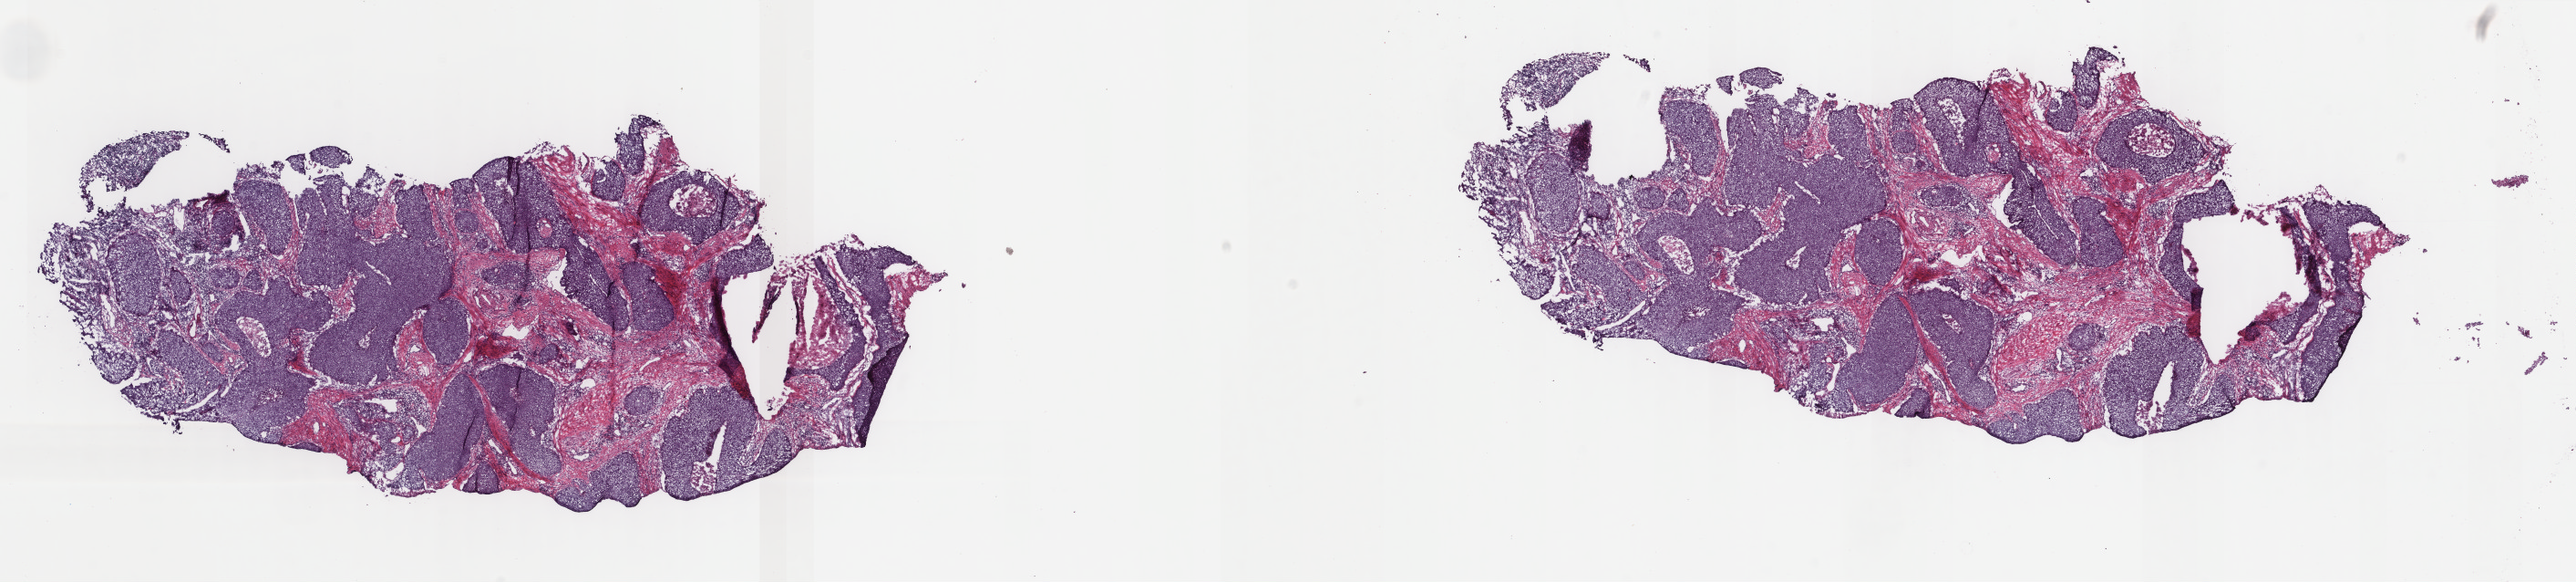
Digitized Hematoxylin and eosin (H&E) stained tissue section (whole slide), a low-resolution overview of the entire scanned area, about 22.4 x 5.1 mm (from a 40x scan), frozen section from the top of the tissue portion, primary tumour sample from the cervix. Patient: female, age at initial diagnosis 58 years. Histologic grade: G3 (poorly differentiated). Pathologist review of this section (percent, as recorded): tumour cells 60%, tumour nuclei 60%, normal cells 0%, stromal cells 35%, necrosis 5%. Inflammatory infiltration, as recorded: lymphocyte infiltration 40%, monocyte infiltration 10%, neutrophil infiltration 30%.
FIGO stage: IIB. Pathologic diagnosis: Squamous cell carcinoma, NOS (cervix uteri).